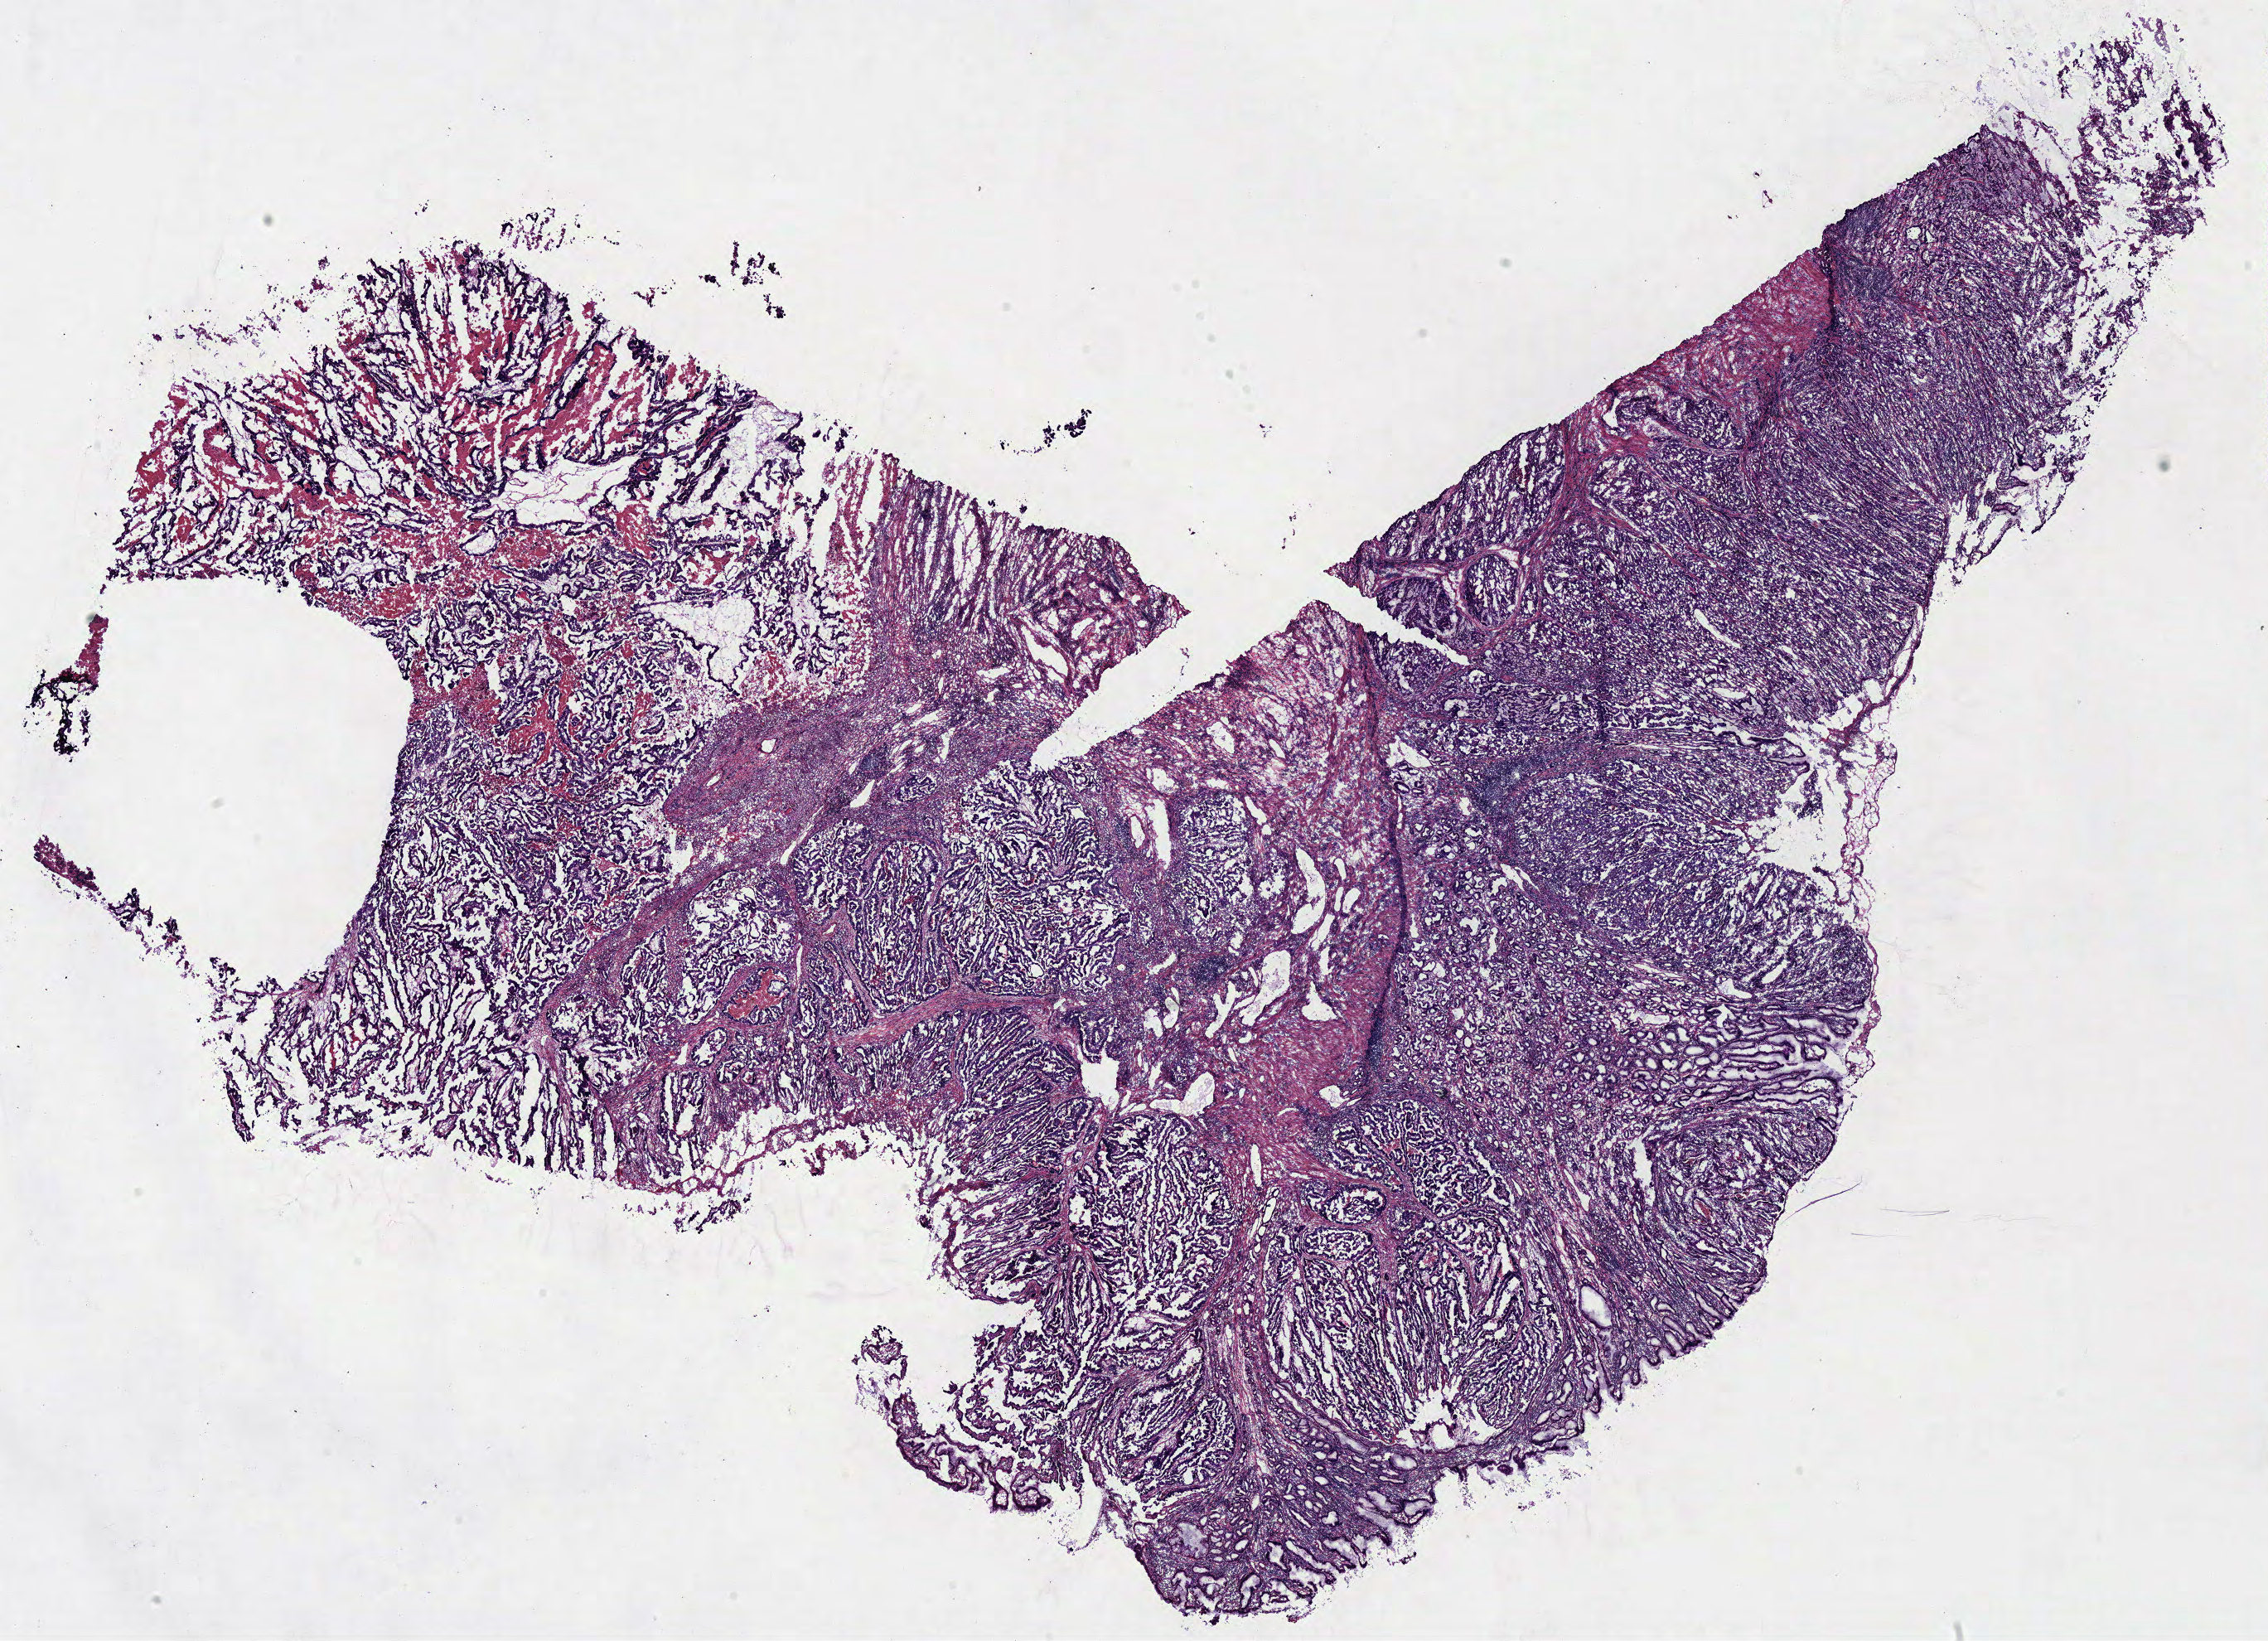
Hematoxylin and eosin (H&E) stained whole-slide image, shown as a low-resolution overview of the whole scanned area (about 21.6 x 15.6 mm, slide scanned at 40x); frozen section from the bottom of the tissue portion; stomach, primary tumour sample. Female, age 51 years at initial diagnosis. Histologic grade: G1 (well differentiated). Pathologist review of this section (percent, as recorded): tumour cells 80%, tumour nuclei 80%, normal cells 0%, stromal cells 10%, necrosis 10%.
Pathologic diagnosis: Papillary adenocarcinoma, NOS (gastric antrum). TNM: T3 N0 M0. AJCC pathologic stage: II (6th edition).